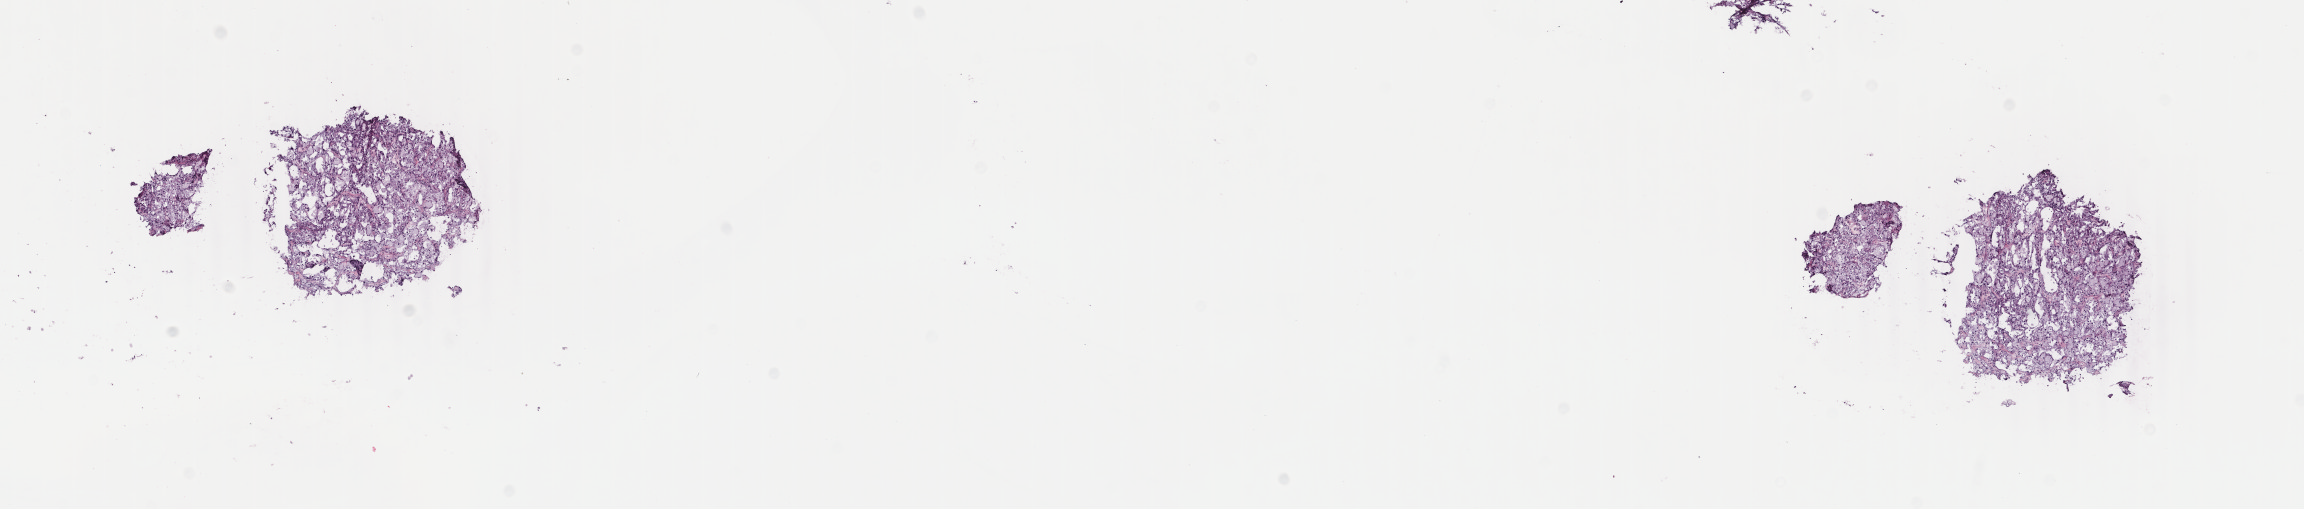
H&E-stained whole-slide image — low-resolution overview of the scanned area, about 18.3 x 4.0 mm (slide scanned at 40x); frozen section; kidney, primary tumour sample. Patient: male, age at initial diagnosis 46 years. Pathologist review of this section (percent, as recorded): tumour cells 70%, tumour nuclei 60%.
Pathologic diagnosis: Papillary adenocarcinoma, NOS.